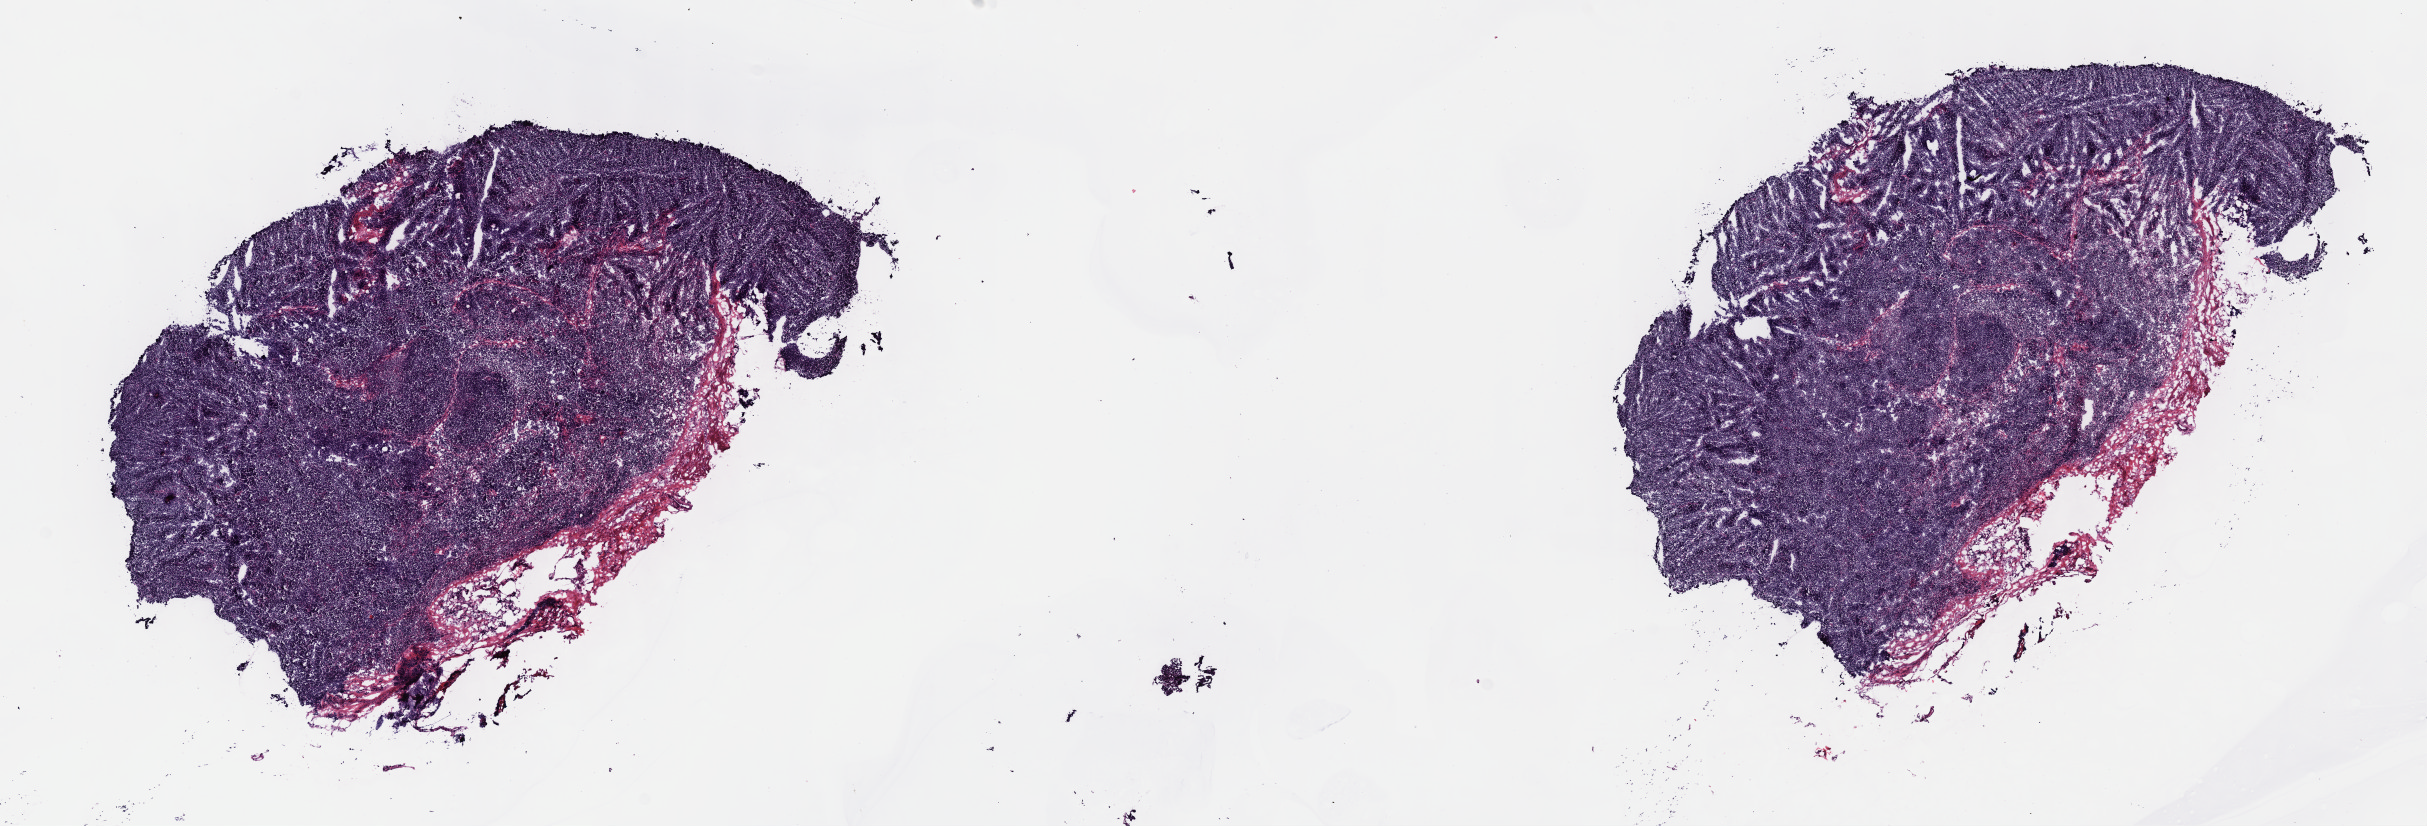
H&E-stained whole-slide image — low-resolution overview of the scanned area, about 19.6 x 6.7 mm (from a 40x scan). Frozen section from the top of the tissue portion. Sample: primary tumour, thymus. Female, age 31 years at initial diagnosis. Pathologist review of this section (percent, as recorded): tumour cells 99%, tumour nuclei 99%, normal cells 0%, stromal cells 1%, necrosis 0%. Inflammatory infiltration, as recorded: lymphocyte infiltration 0%, monocyte infiltration 0%, neutrophil infiltration 0%.
Pathologic diagnosis: Thymoma, type B1, malignant.